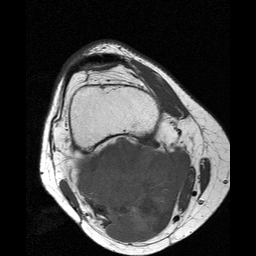
MRI of an extremity soft-tissue mass, one axial slice; position 15 of 25 along the scan axis; 256 × 256 image matrix, field of view 160 × 160 mm. Female patient. From the clinical record (not read from this slice): histological type: liposarcoma; site of the primary tumour: right thigh.
Structures marked on this image (outlined manually by an expert reader):
- gross tumour volume (mass): bounding box (x1, y1, x2, y2) in pixels: (72, 137, 192, 243)